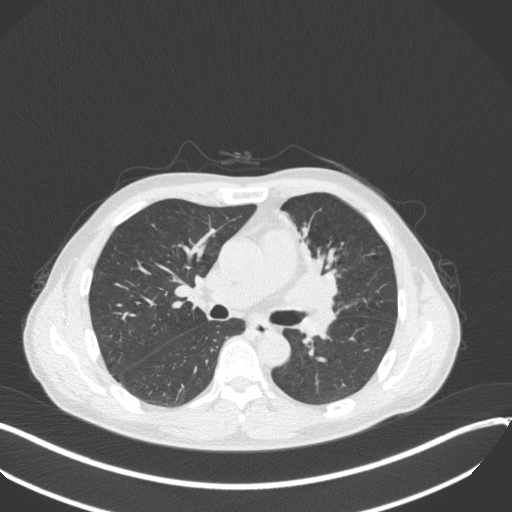
Chest CT, one axial slice. Slice 194 of 411 in the series (ordered by position). 120 kVp. Lung window (W 1500 / L -600 HU). 1 mm slice thickness. 512 × 512 image matrix, field of view 400 × 400 mm. Patient: male, 56 years. Case-level facts recorded for this patient, not image findings: clinical TNM (as recorded): T2a N0 M0.
Structures marked on this image (rectangle marked by the reading radiologist):
- lung tumour (recorded histology: squamous cell carcinoma): bounding box (x1, y1, x2, y2) in pixels: (284, 233, 343, 311)